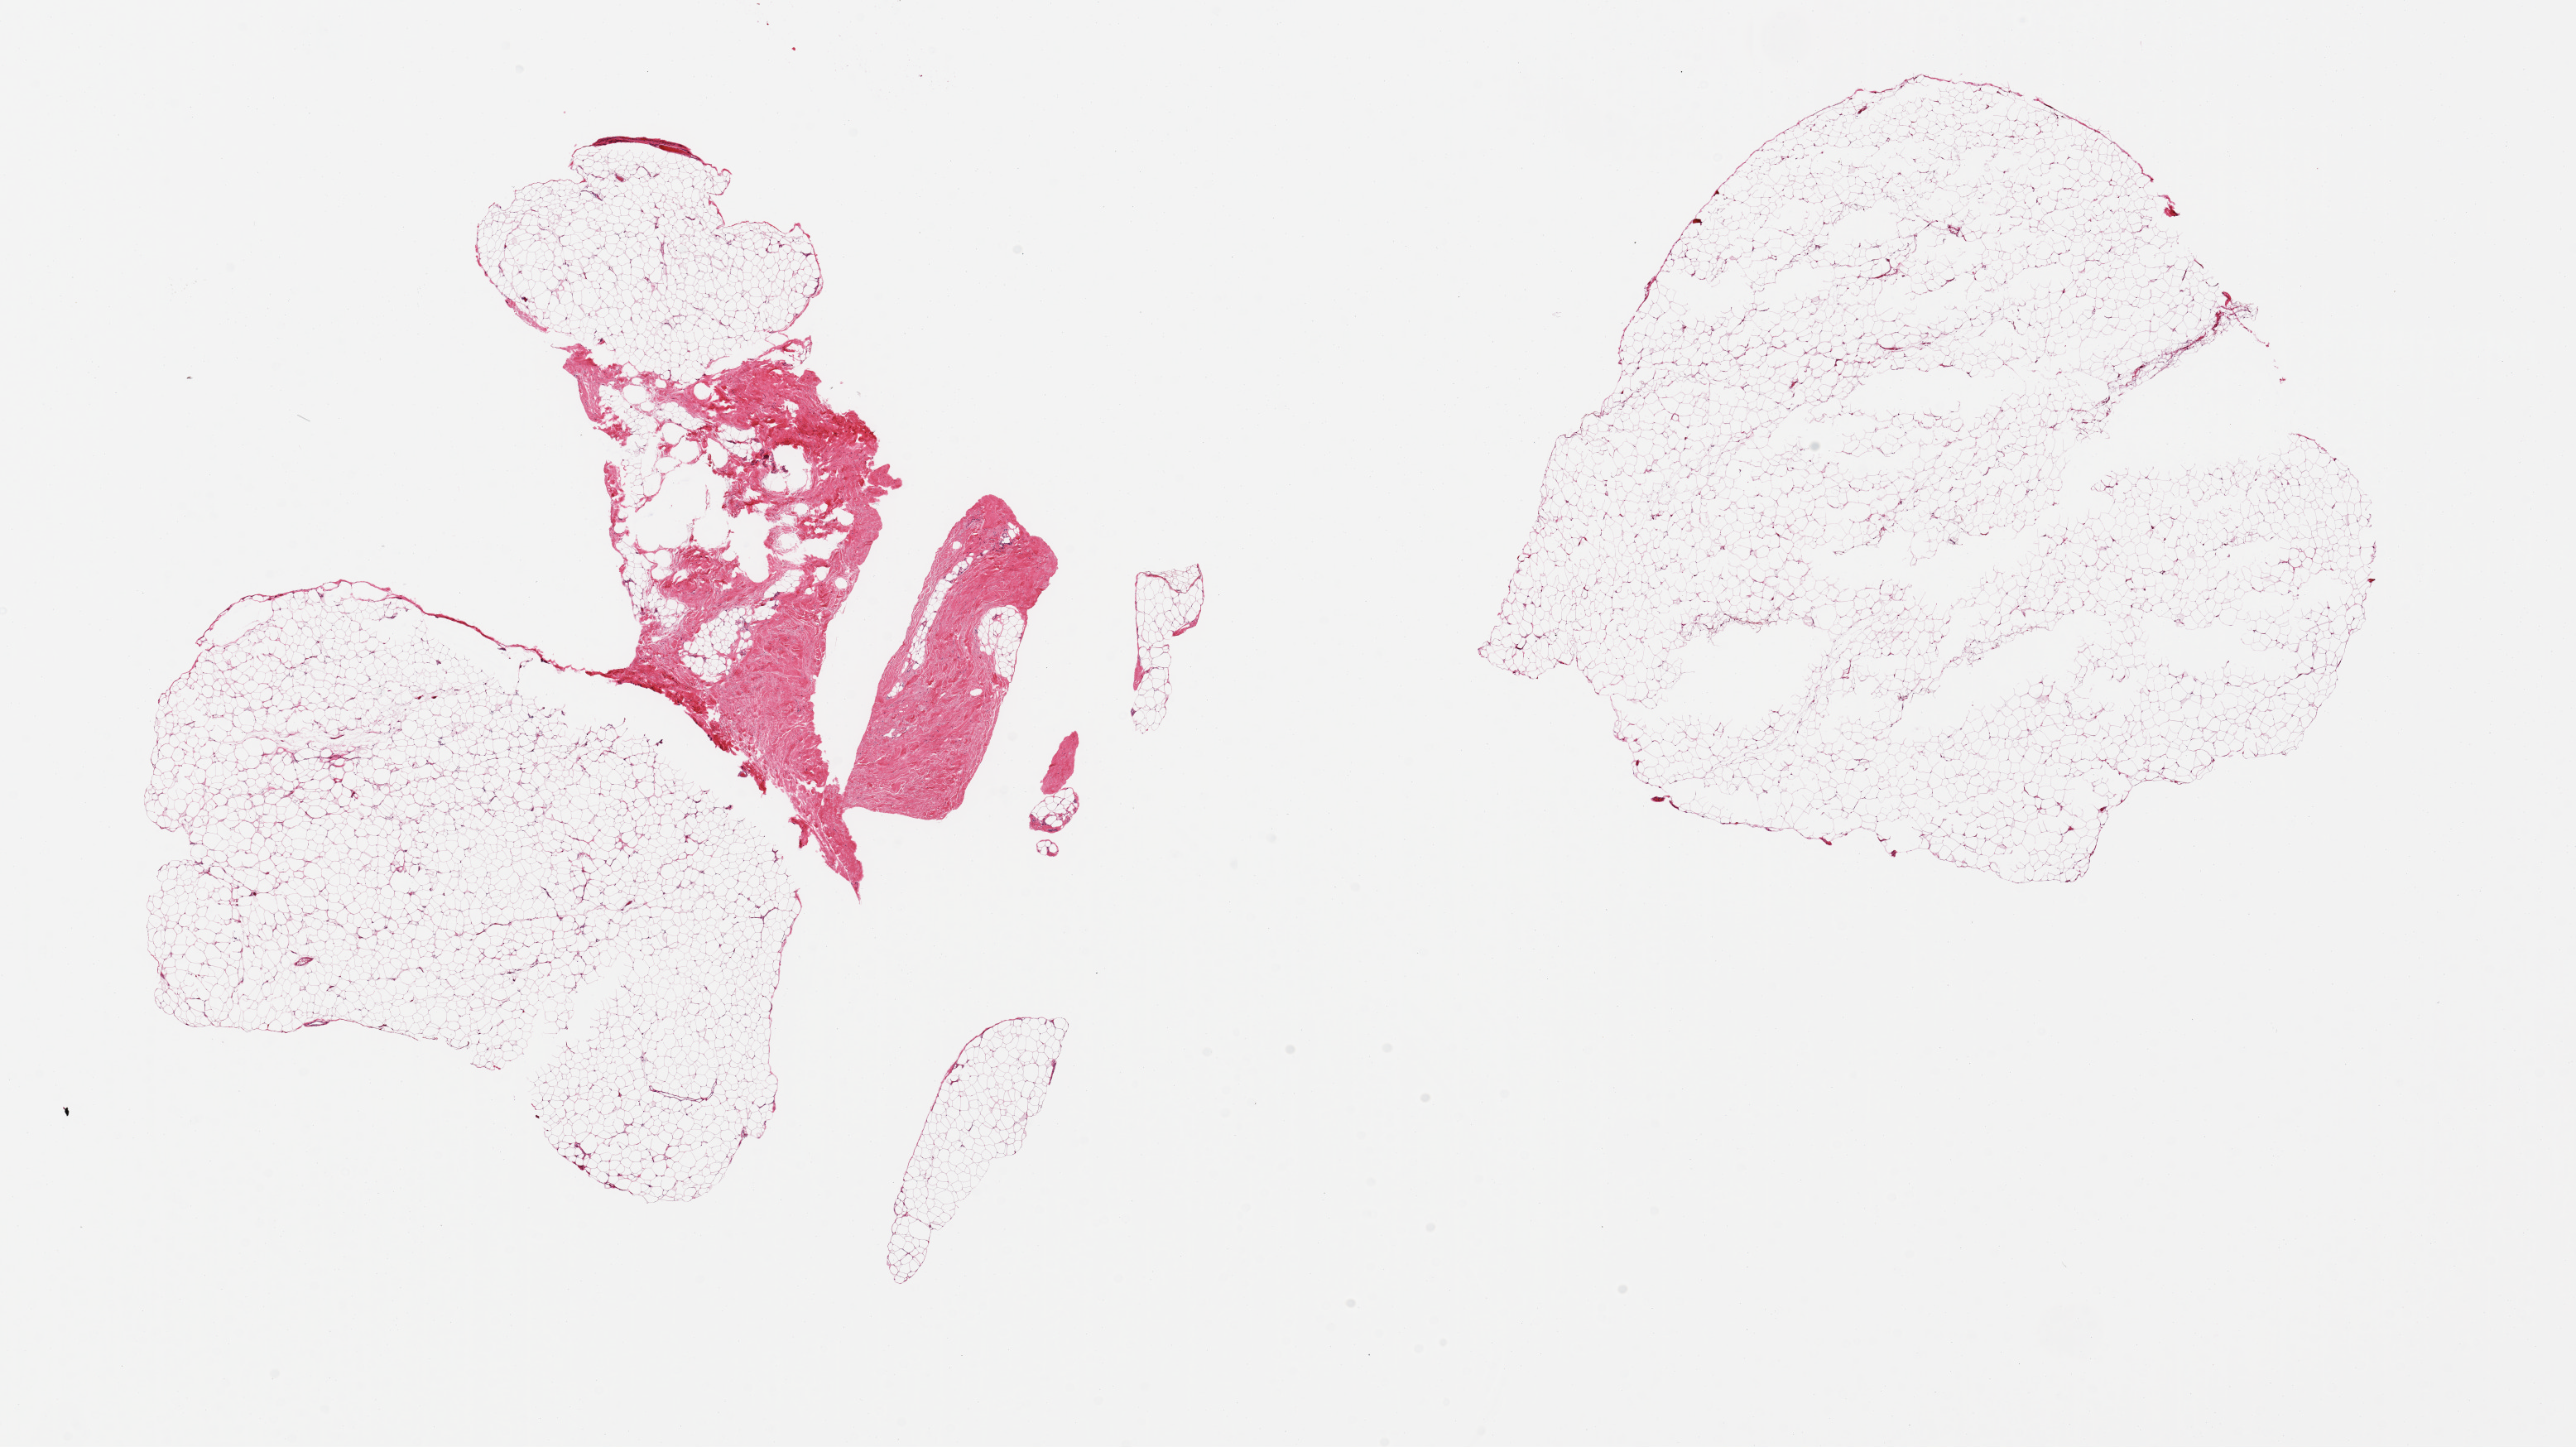
Hematoxylin and eosin (H&E) whole-slide image, shown as a low-resolution overview of the whole scanned area (about 24.6 x 13.8 mm); PAXgene-fixed, paraffin-embedded tissue; sampled site (target tissue): adipose tissue; donor tissue sample. Donor: female.
Review note (as recorded): 2 pieces; 1 piece includes central defects (?poor fixation); 2nd is ~30% fibrous.